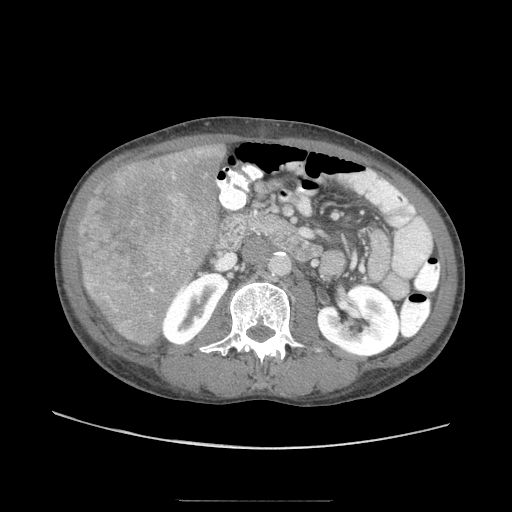
Contrast-enhanced abdominal CT (liver protocol), one axial slice; slice 22 of 103 in the series (ordered by position); soft-tissue window (W 400 / L 40 HU); 512 × 512 image matrix, field of view 380 × 380 mm. From the clinical record (not read from this slice): diagnosis: hepatocellular carcinoma (patient treated with transarterial chemoembolisation; whether this scan precedes or follows treatment is not stated here); TNM stage (as recorded): Stage-IIIA; Child-Pugh class: A; tumour differentiation: moderately differentiated; tumour nodularity: multinodular.
Outlined on this slice (semi-automatic segmentation, software-assisted and operator-edited):
- liver parenchyma outside the tumour (the mass and vessels are separate outlines, so this box may not span the whole liver): bounding box [x1, y1, x2, y2] px = [82, 138, 226, 346]
- mass: [76, 158, 198, 314]